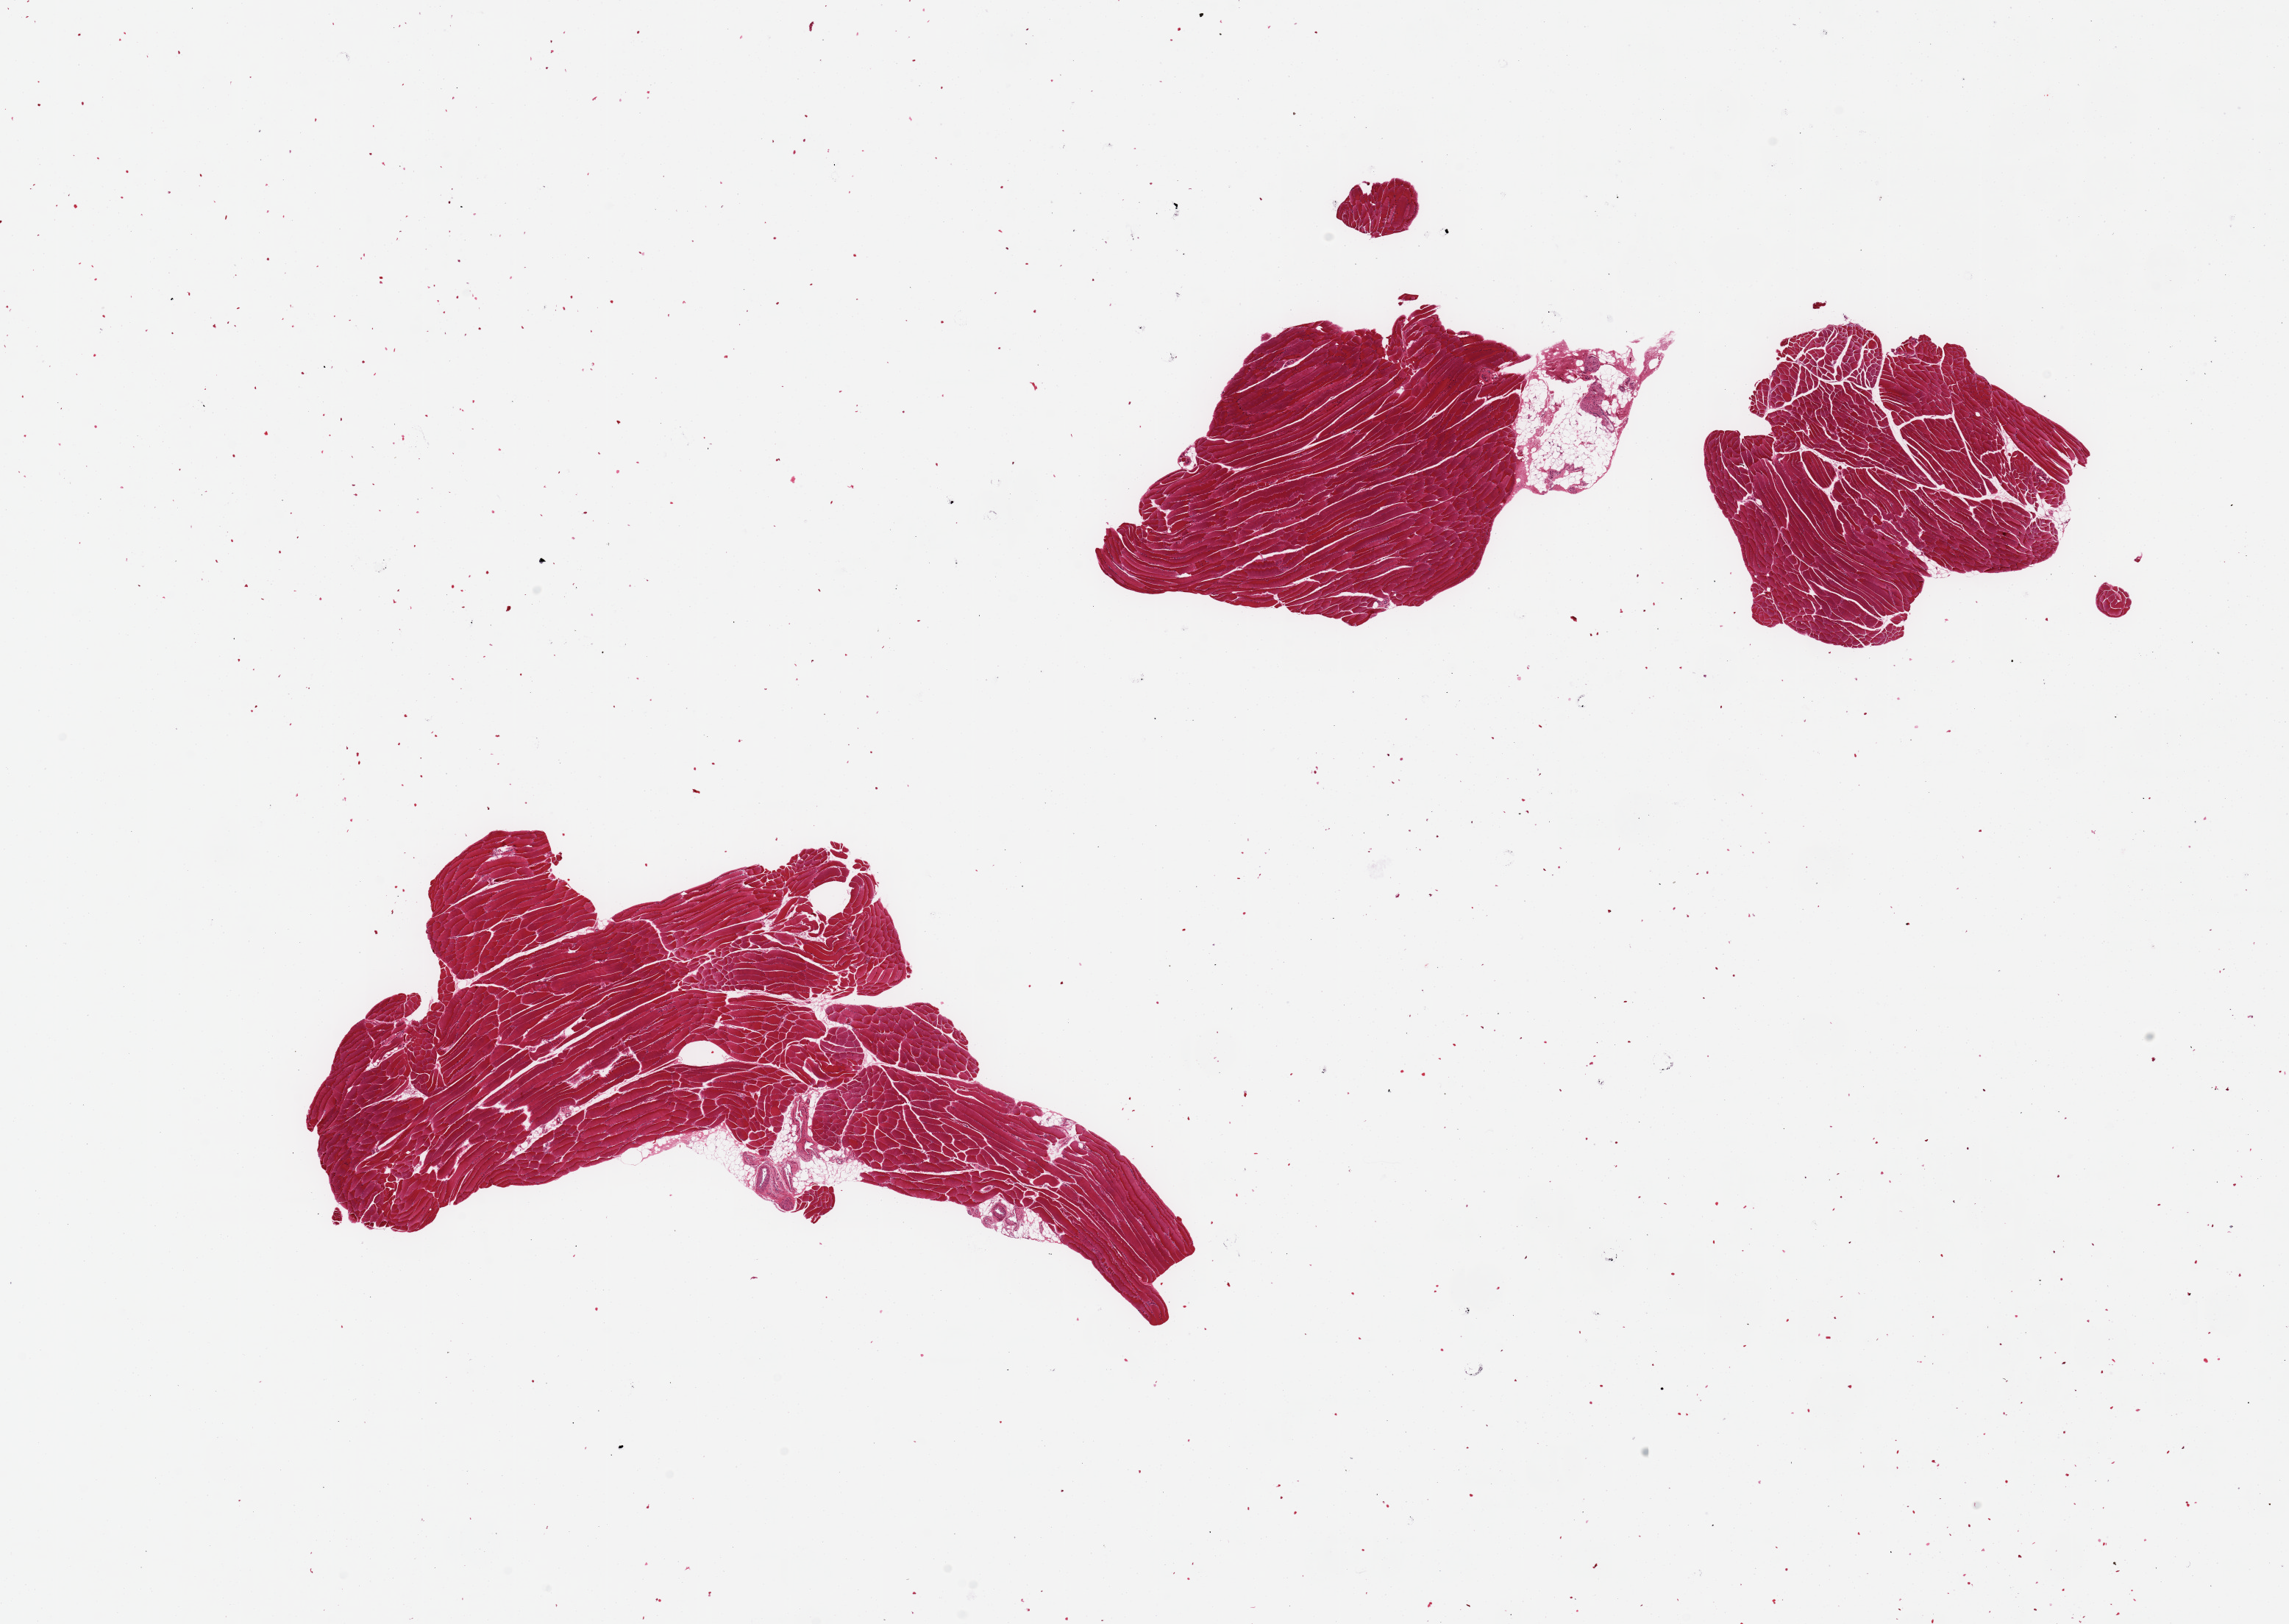
Whole-slide image, H&E stain, shown as a low-resolution overview of the whole scanned area (about 24.6 x 17.5 mm, from a 20x scan). PAXgene-fixed, paraffin-embedded tissue. Section of skeletal muscle (target tissue). Tissue donor sample. Female donor.
Reviewer comment on this tissue sample: 2 pieces; small amounts of external fat.